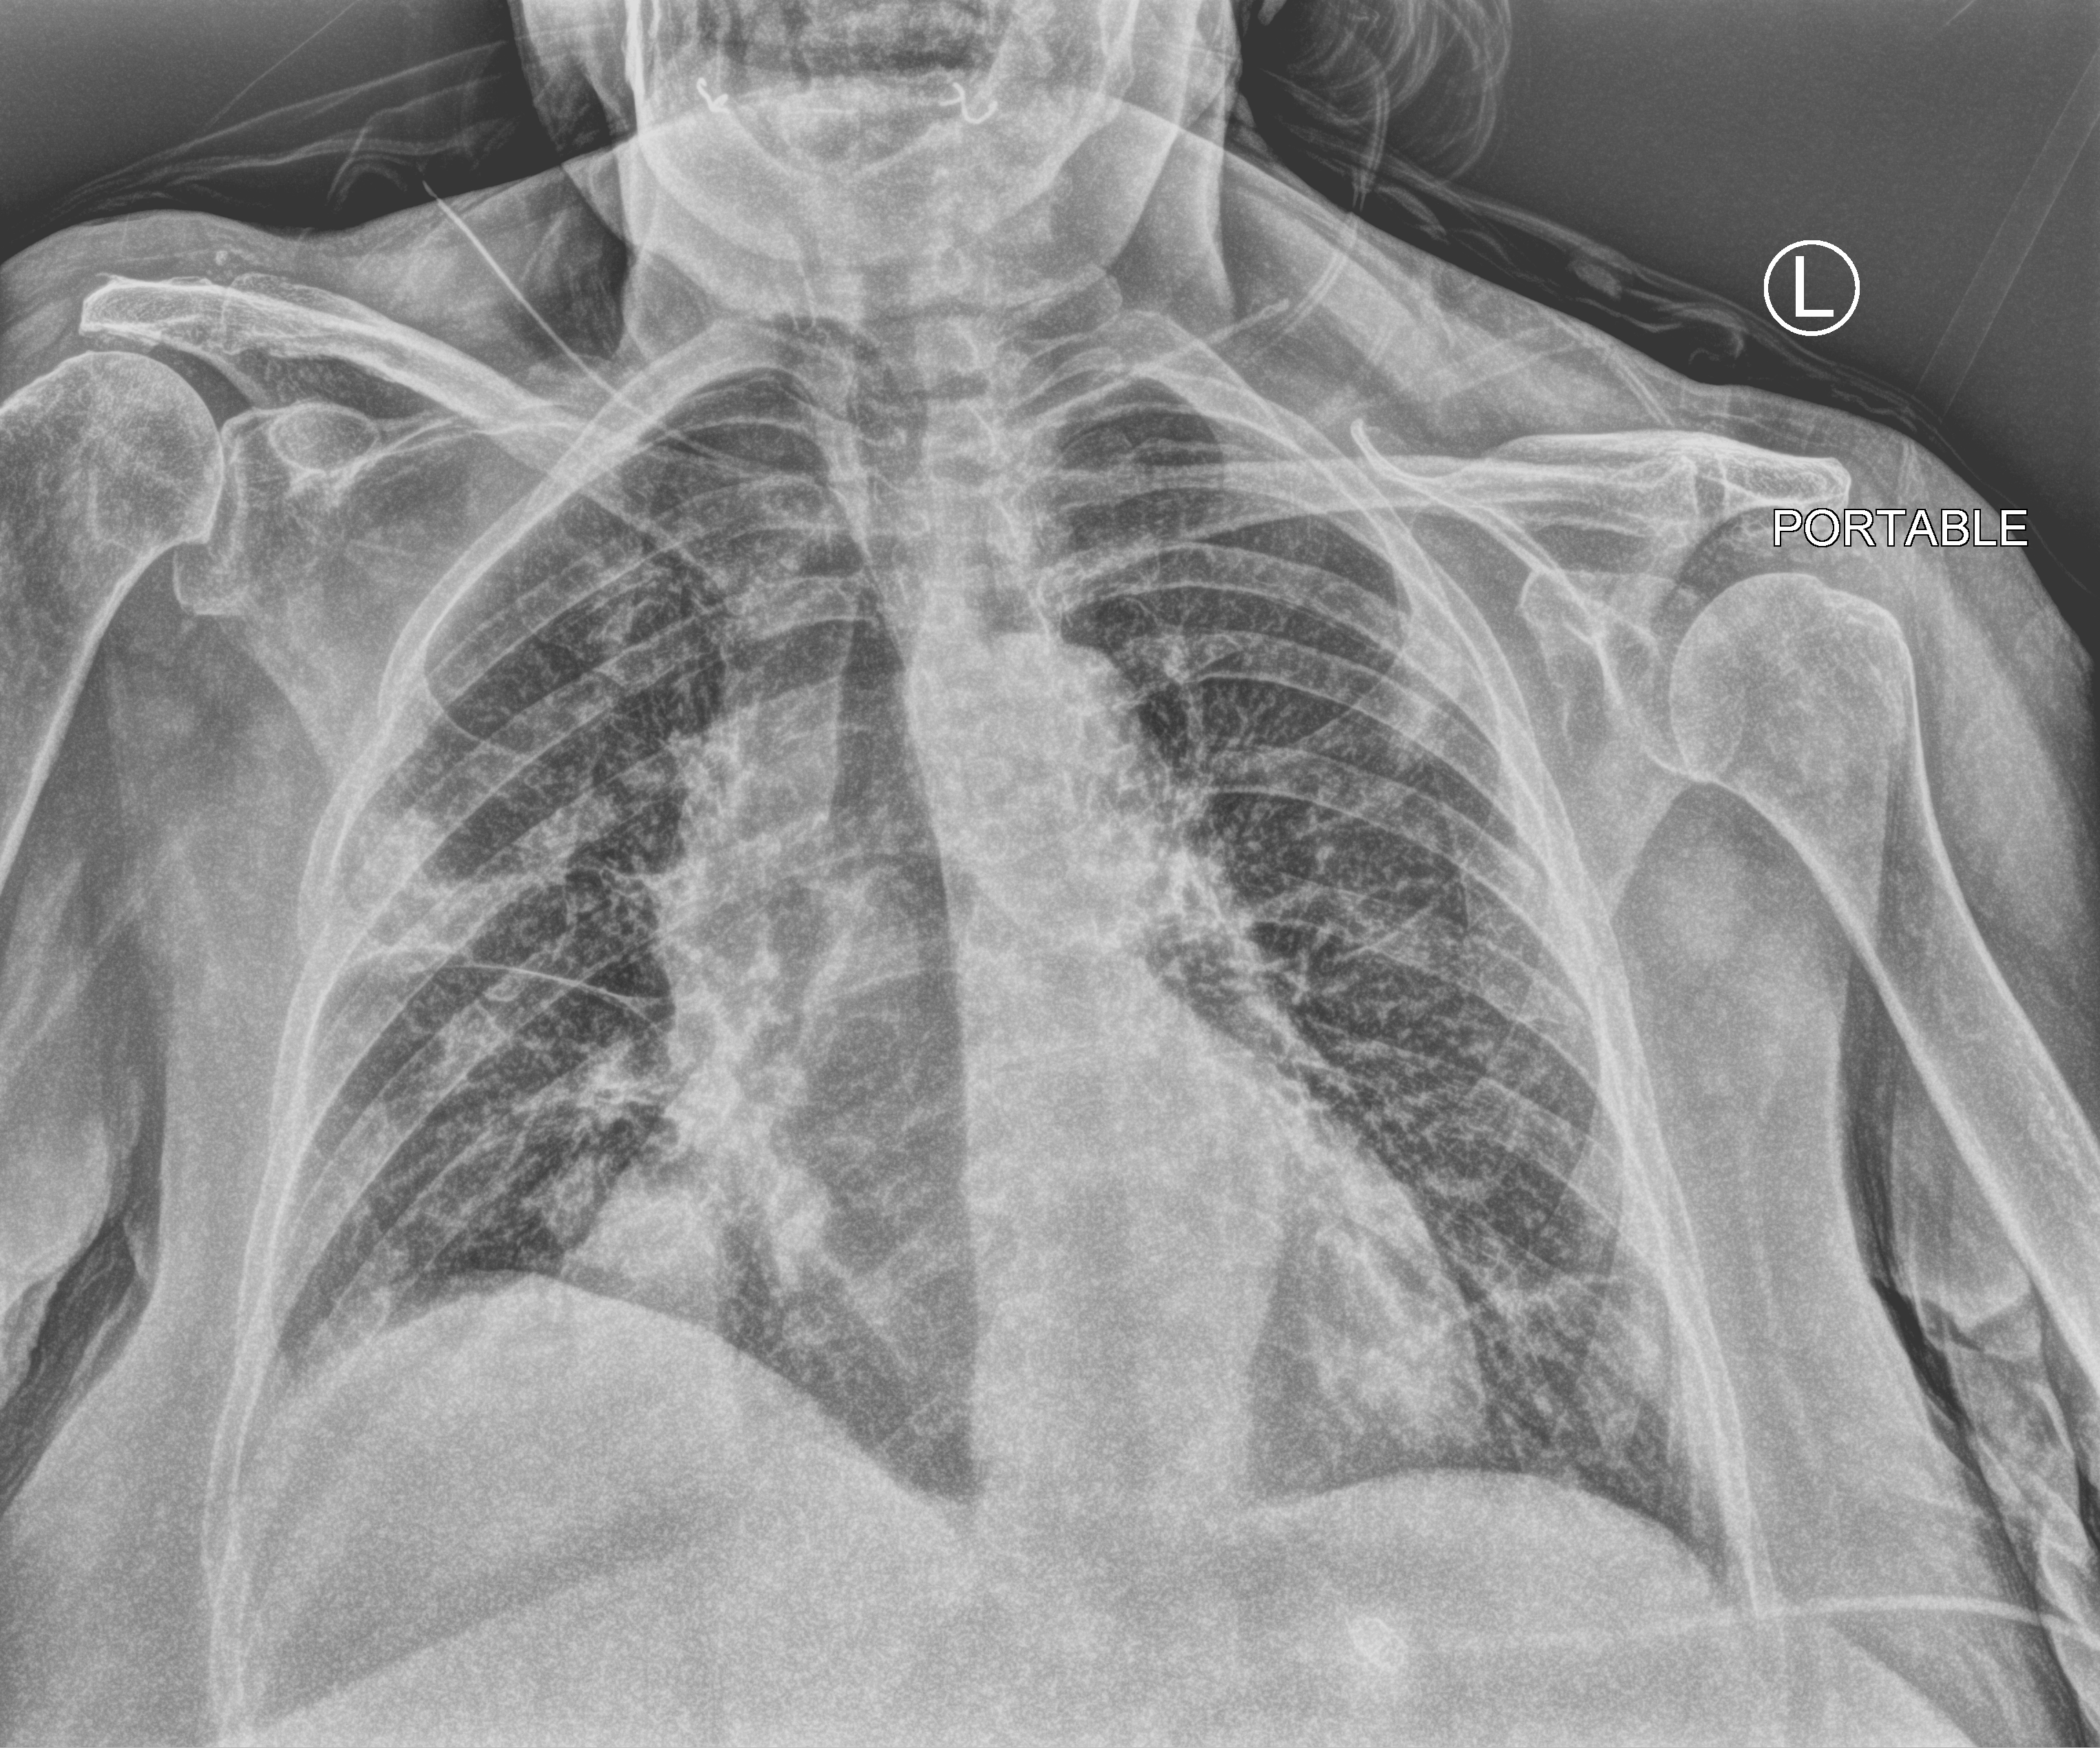
Chest X-ray (portable), anteroposterior (AP) projection. Female patient hospitalised with COVID-19, age 75–90 years.
Hospital-stay facts (about this admission, not read from this image; timing relative to this image not recorded): admitted to intensive care during this hospital stay: no; mechanically ventilated during this hospital stay: no.